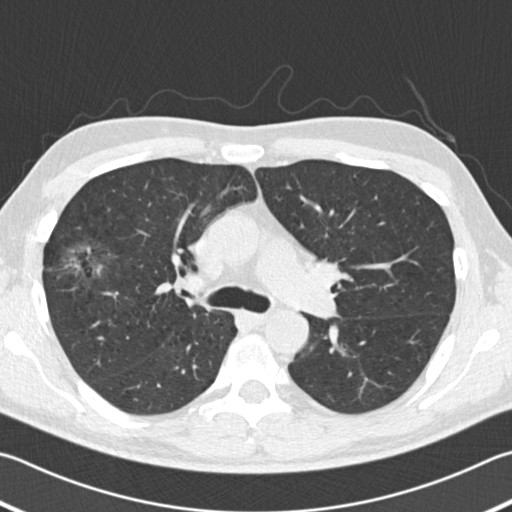
Low-dose screening chest CT, axial slice; second screening round (one year after baseline); lung window (W 1500 / L -600 HU); 120 kVp. Male, age 56 years at enrolment. Former smoker at enrolment.
Expert-annotated lung lesion, bounding box <45,232,124,297> (left, top, right, bottom; pixels). Reader record for this screening exam (exam-level; its link to the box is not recorded): non-calcified nodule or mass ≥4 mm, right upper lobe, 18 × 14 mm, spiculated (stellate) margins, soft tissue attenuation, pre-existing on the prior screen: yes; interval growth: yes. Participant outcome: lung cancer diagnosed 42 days after this screen — bronchiolo-alveolar adenocarcinoma, NOS, right upper lobe, well differentiated (G1), stage IIB (AJCC 6th edition), 30 mm at pathology.